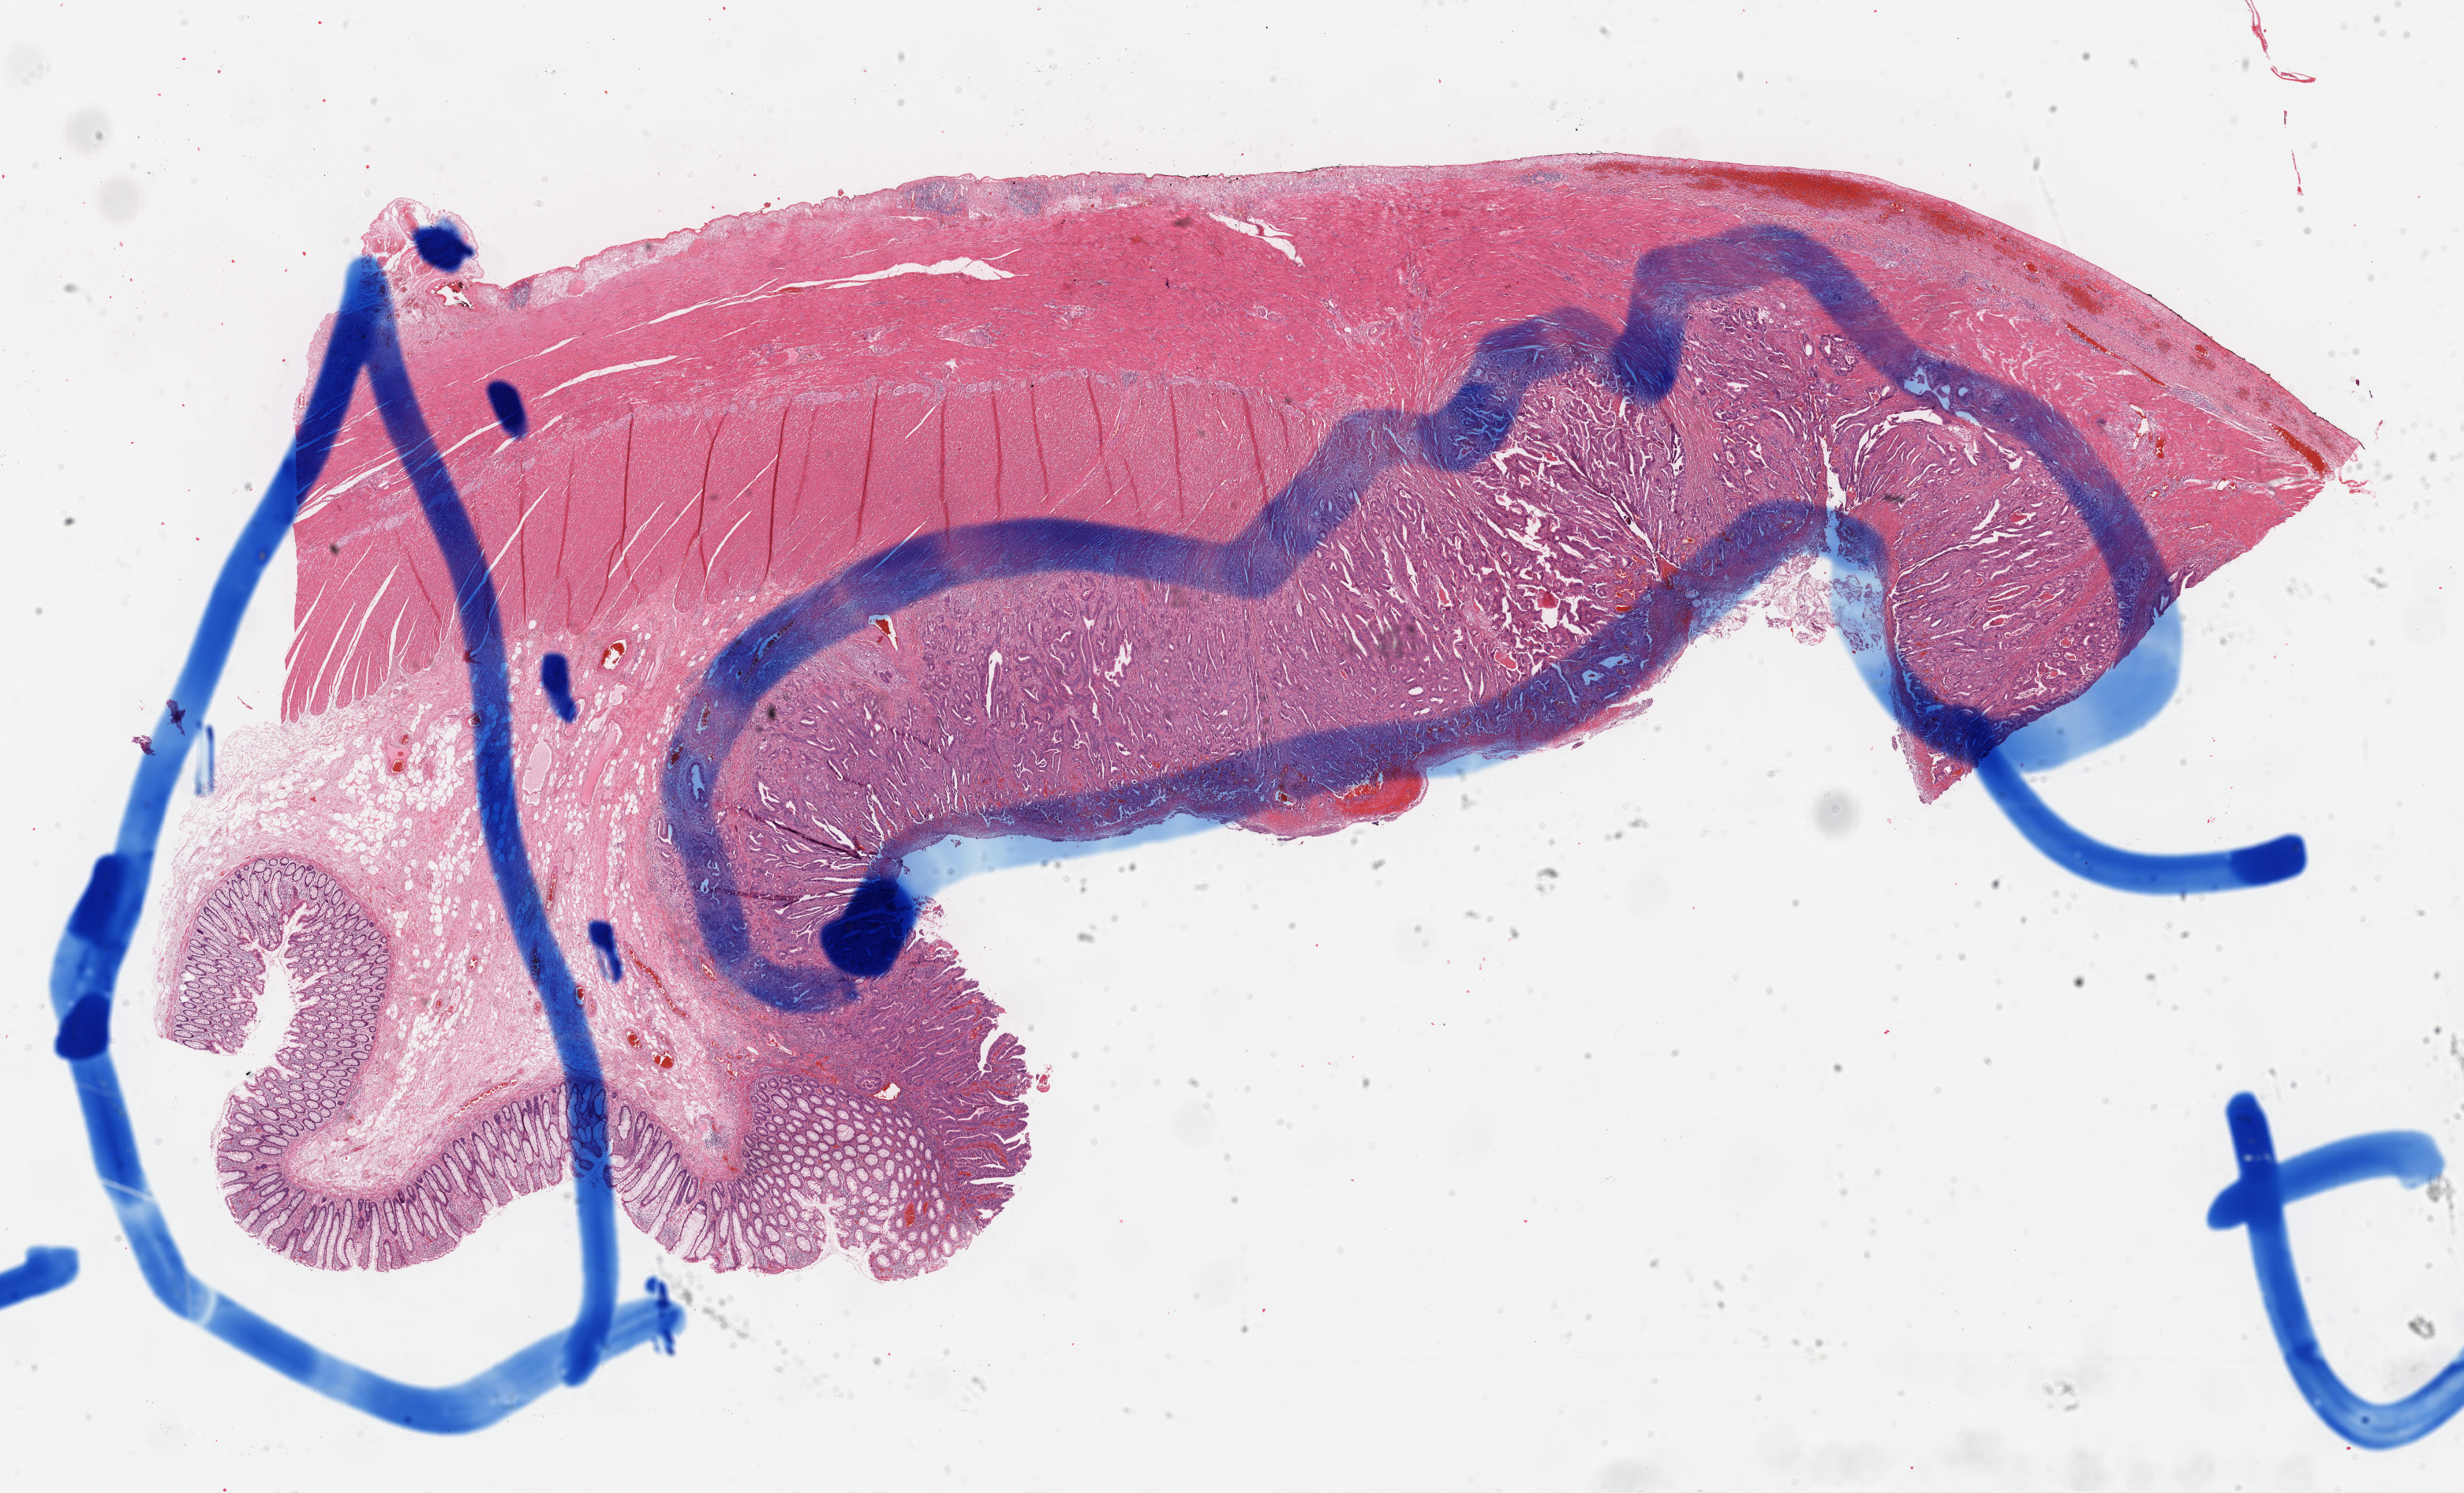
Whole-slide histology image, H&E-stained, shown as a low-resolution overview of the whole scanned area (about 24.7 x 14.9 mm, slide scanned at 40x); formalin-fixed paraffin-embedded (FFPE) diagnostic section; primary tumour sample from the rectum. Patient: female, age at initial diagnosis 56 years.
Diagnosis: Adenocarcinoma, NOS. AJCC pathologic stage: IIA.